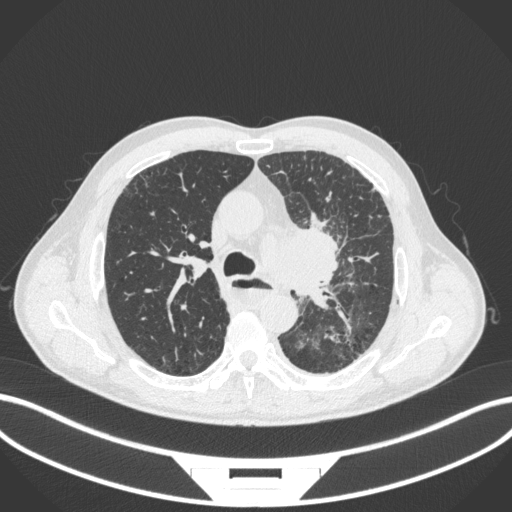
Chest CT, one axial slice. Slice 258 of 411 in the series (ordered by position). Reconstruction kernel B31f. Lung window (W 1500 / L -600 HU). 1 mm slice thickness. 512 × 512 image matrix. Male patient, age 57 years. Case-level facts recorded for this patient, not image findings: clinical TNM (as recorded): T2a N1 M0.
Structures marked on this image (rectangle marked by the reading radiologist):
- lung tumour (recorded histology: squamous cell carcinoma): bounding box [x1, y1, x2, y2] px = [261, 224, 348, 308]